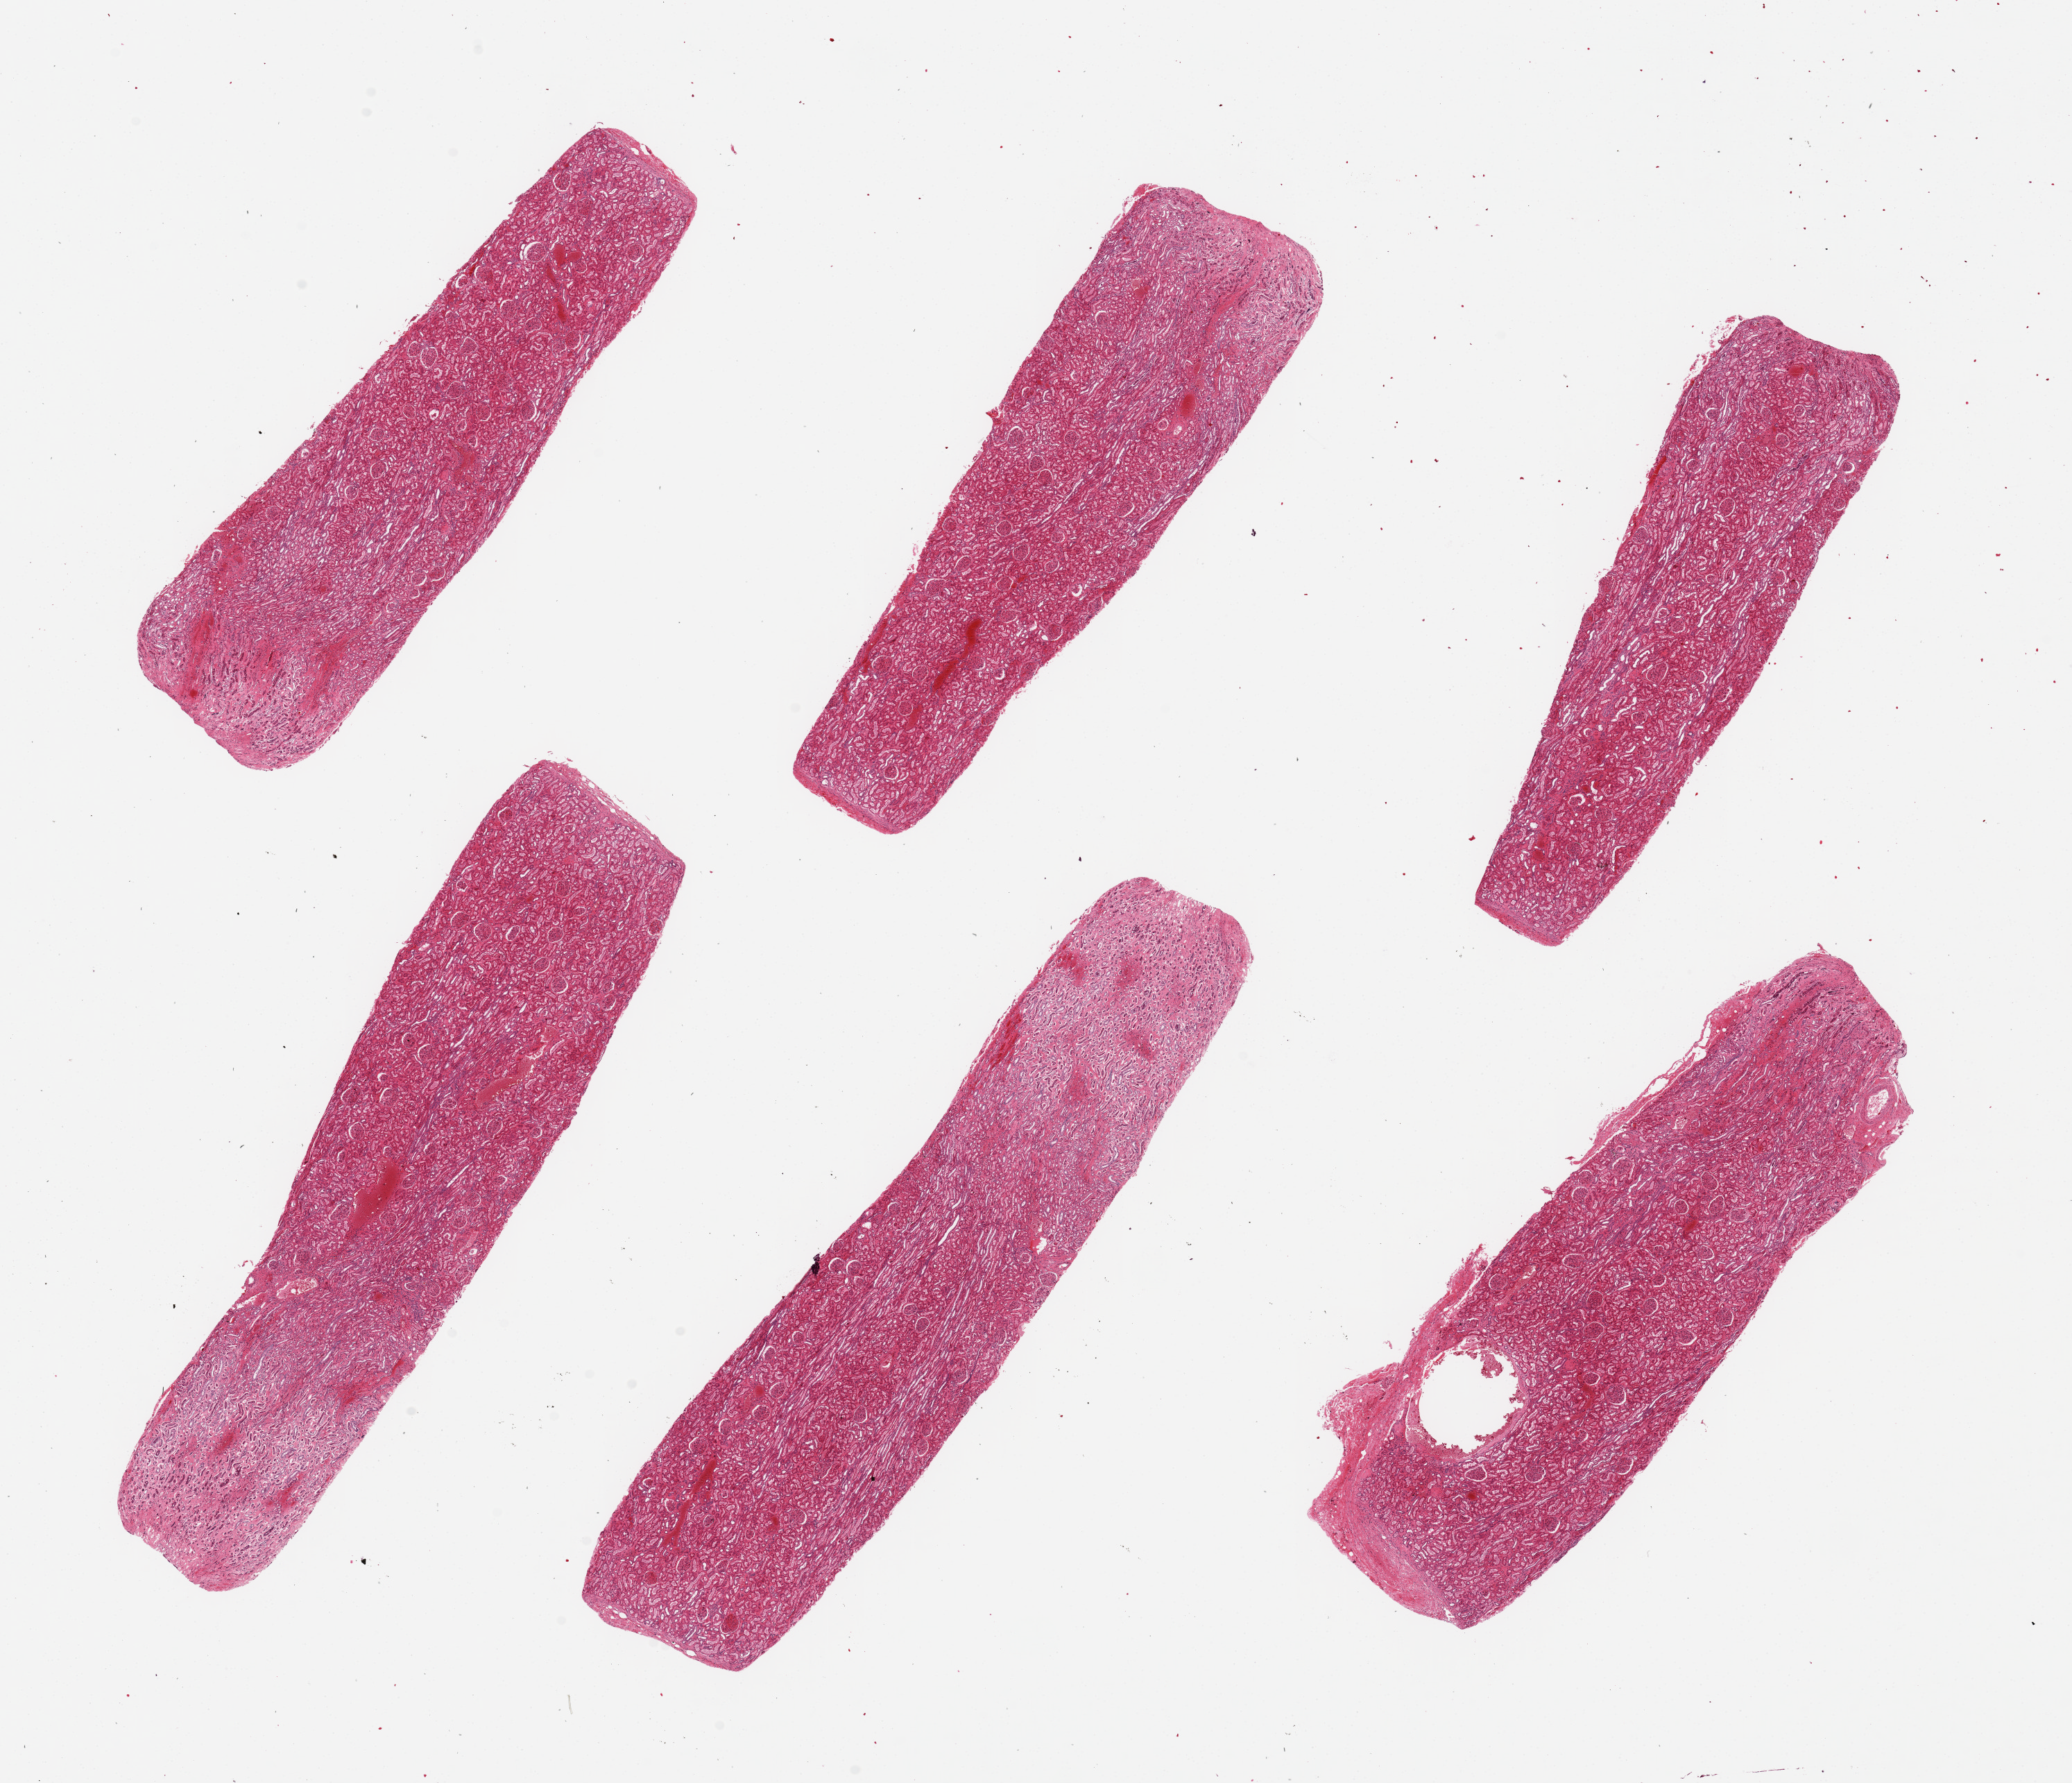
Whole-slide image, hematoxylin and eosin (H&E) stain, brightfield, whole scanned area (about 23.6 x 20.3 mm) shown as a low-resolution overview, PAXgene-fixed, paraffin-embedded tissue, section of renal cortex (target tissue), tissue donor sample. Donor: male.
Reviewer comment on this tissue sample: 6 pieces ~8x2mm, remarkabley well-preserved.